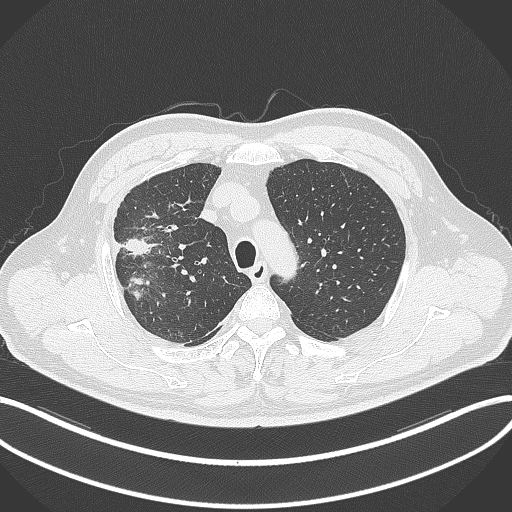
Chest CT, one axial slice; position 266 of 348 along the scan axis; 120 kVp; lung window (W 1500 / L -600 HU); 1 mm slice thickness; 512 × 512 image matrix, field of view 400 × 400 mm. Male patient, age 55 years. Case-level facts recorded for this patient, not image findings: clinical TNM (as recorded): T3 N2 M1.
Annotated regions visible in this slice (bounding box drawn by a radiologist):
- lung tumour (recorded histology: adenocarcinoma): bounding box <119,232,159,305> (left, top, right, bottom; pixels)